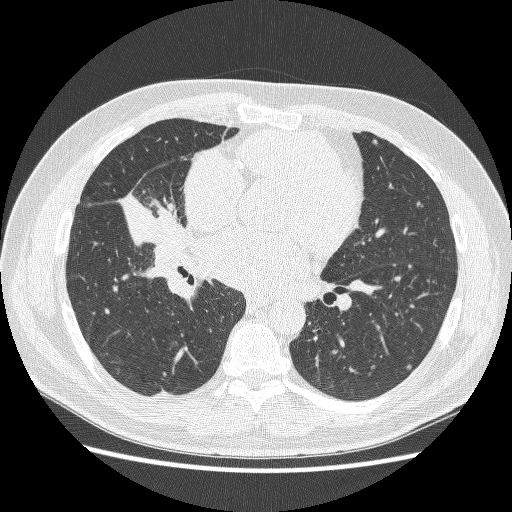
Chest CT (low-dose screening protocol), one axial image, first (baseline) screen, lung window (W 1500 / L -600 HU), lung (sharp) reconstruction kernel (BONE), slice 131 of 251 in the series, 512 × 512 image matrix. Male participant, aged 59 years at enrolment.
Lesion marked by an expert reader, bounding box (x1, y1, x2, y2) in pixels: (116, 174, 196, 254). No non-calcified nodule or mass ≥4 mm was recorded by the screening reader at this exam. Lung cancer was diagnosed 24 days after this screen: adenocarcinoma, NOS, right middle lobe, poorly differentiated (G3), stage IV (AJCC 6th edition), 54 mm at pathology.